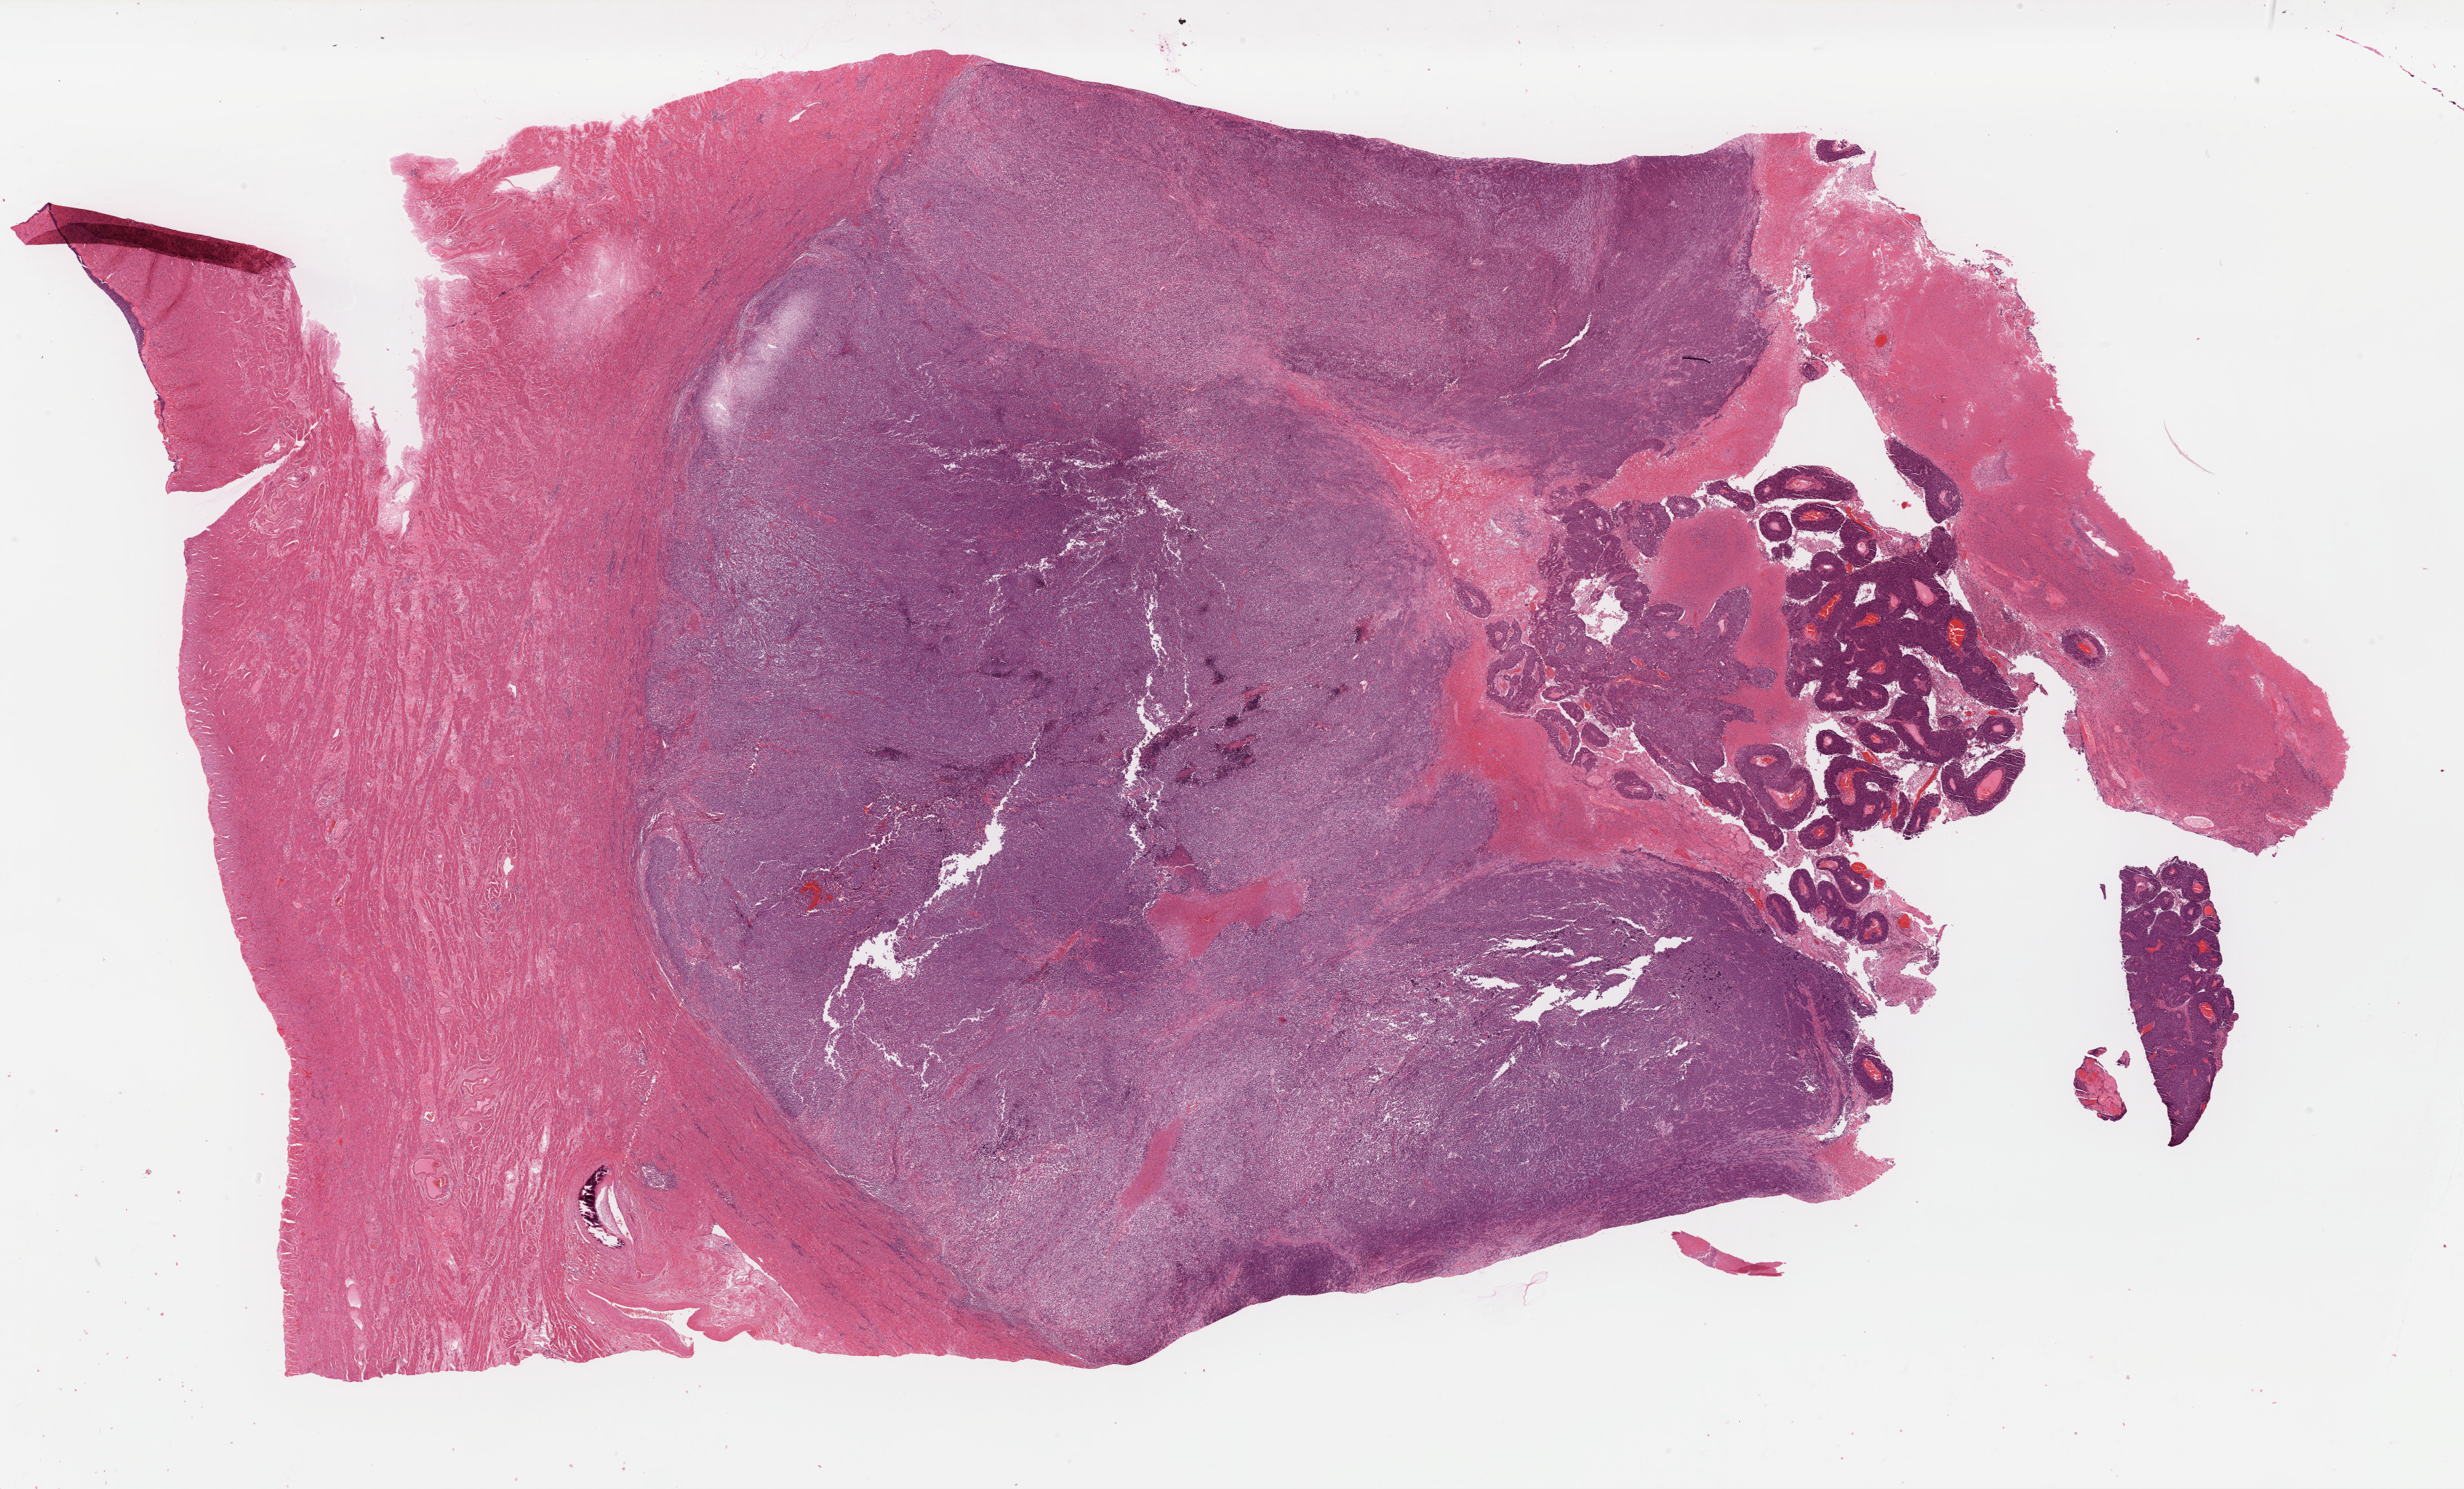
Whole-slide histology image, H&E-stained — a low-resolution overview of the entire scanned area, about 28.2 x 17.0 mm (slide scanned at 40x); formalin-fixed paraffin-embedded (FFPE) diagnostic section; sample: primary tumour, uterus. Female patient; age at initial diagnosis 74 years. Histologic grade: G3 (poorly differentiated).
FIGO stage: IB. Diagnosis: Endometrioid adenocarcinoma, NOS (endometrium).